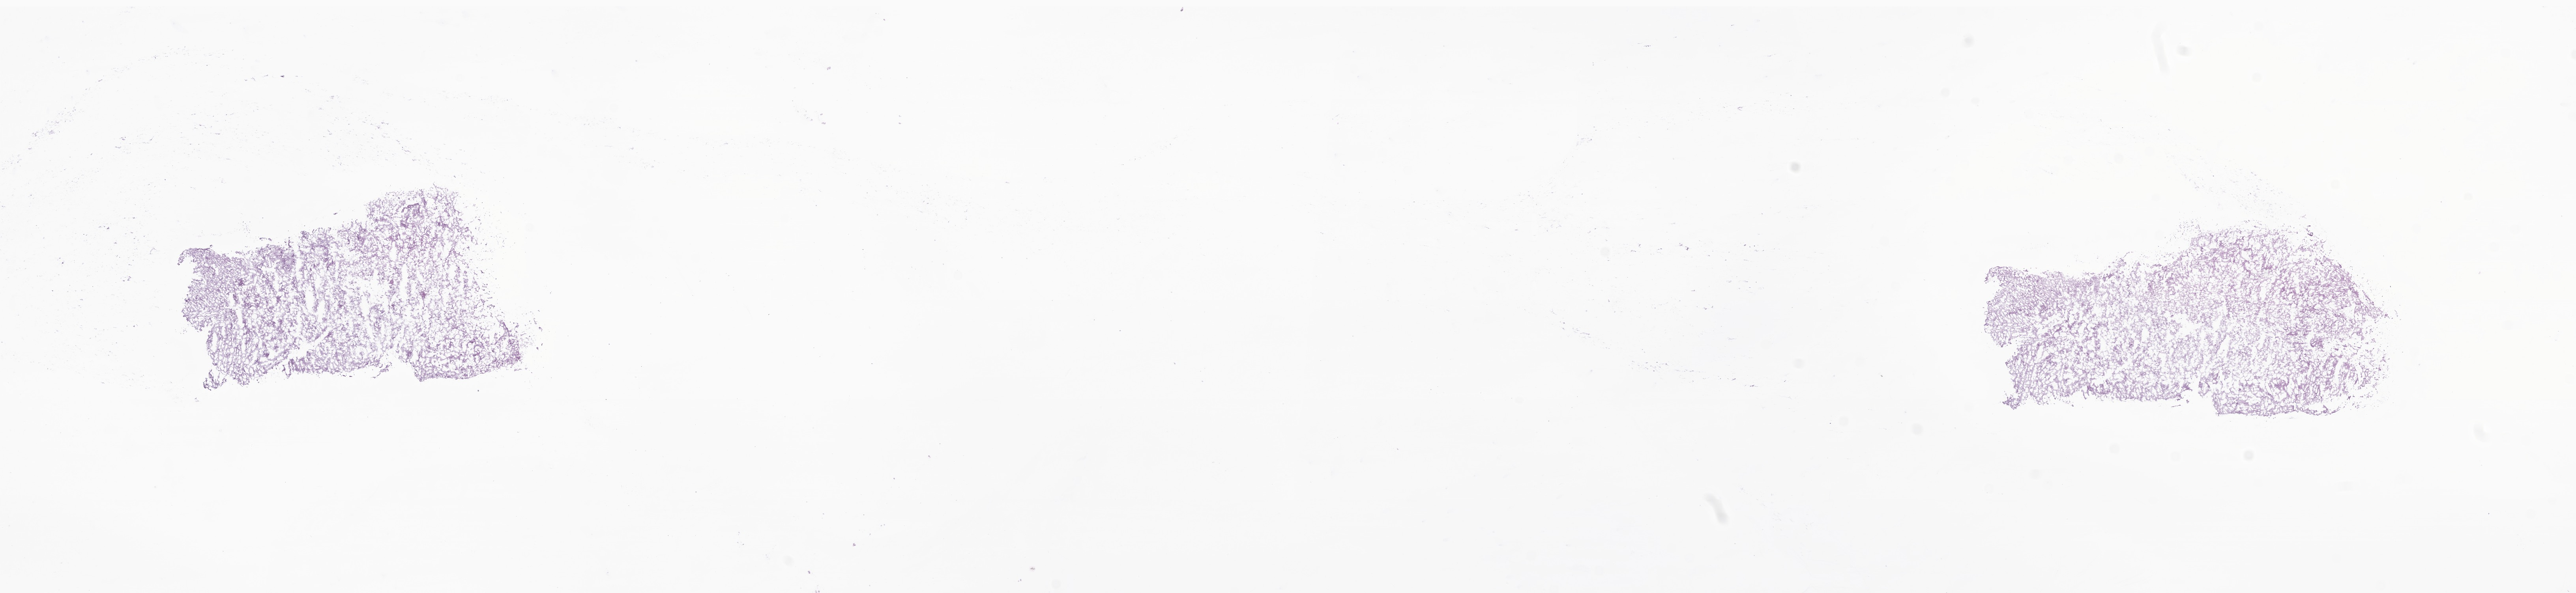
H&E whole-slide image of tumor tissue from the brain, shown as a low-resolution overview of the whole scanned area (about 27.5 x 6.3 mm). Cryosection (OCT / tissue freezing medium). Female patient, age 38 months (3 years 2 months).
Diagnosis: Pilocytic astrocytoma.